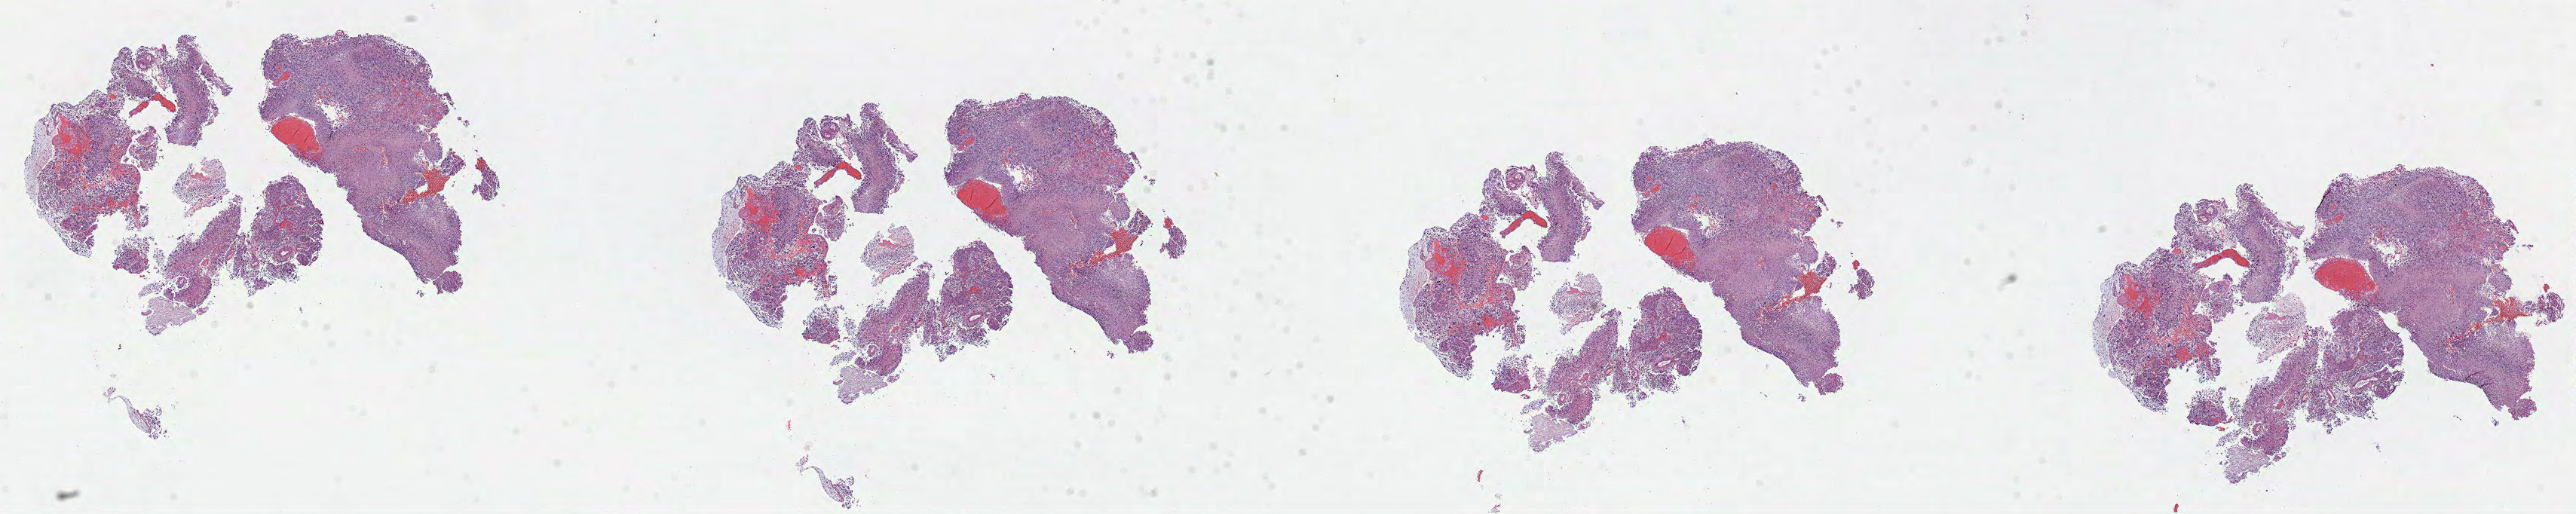
H&E-stained whole-slide image — a low-resolution overview of the entire scanned area, about 27.6 x 5.5 mm (from a 40x scan); formalin-fixed paraffin-embedded (FFPE) diagnostic section; sample: primary tumour, brain. Patient: female, age at initial diagnosis 45 years.
• pathologic diagnosis: Glioblastoma